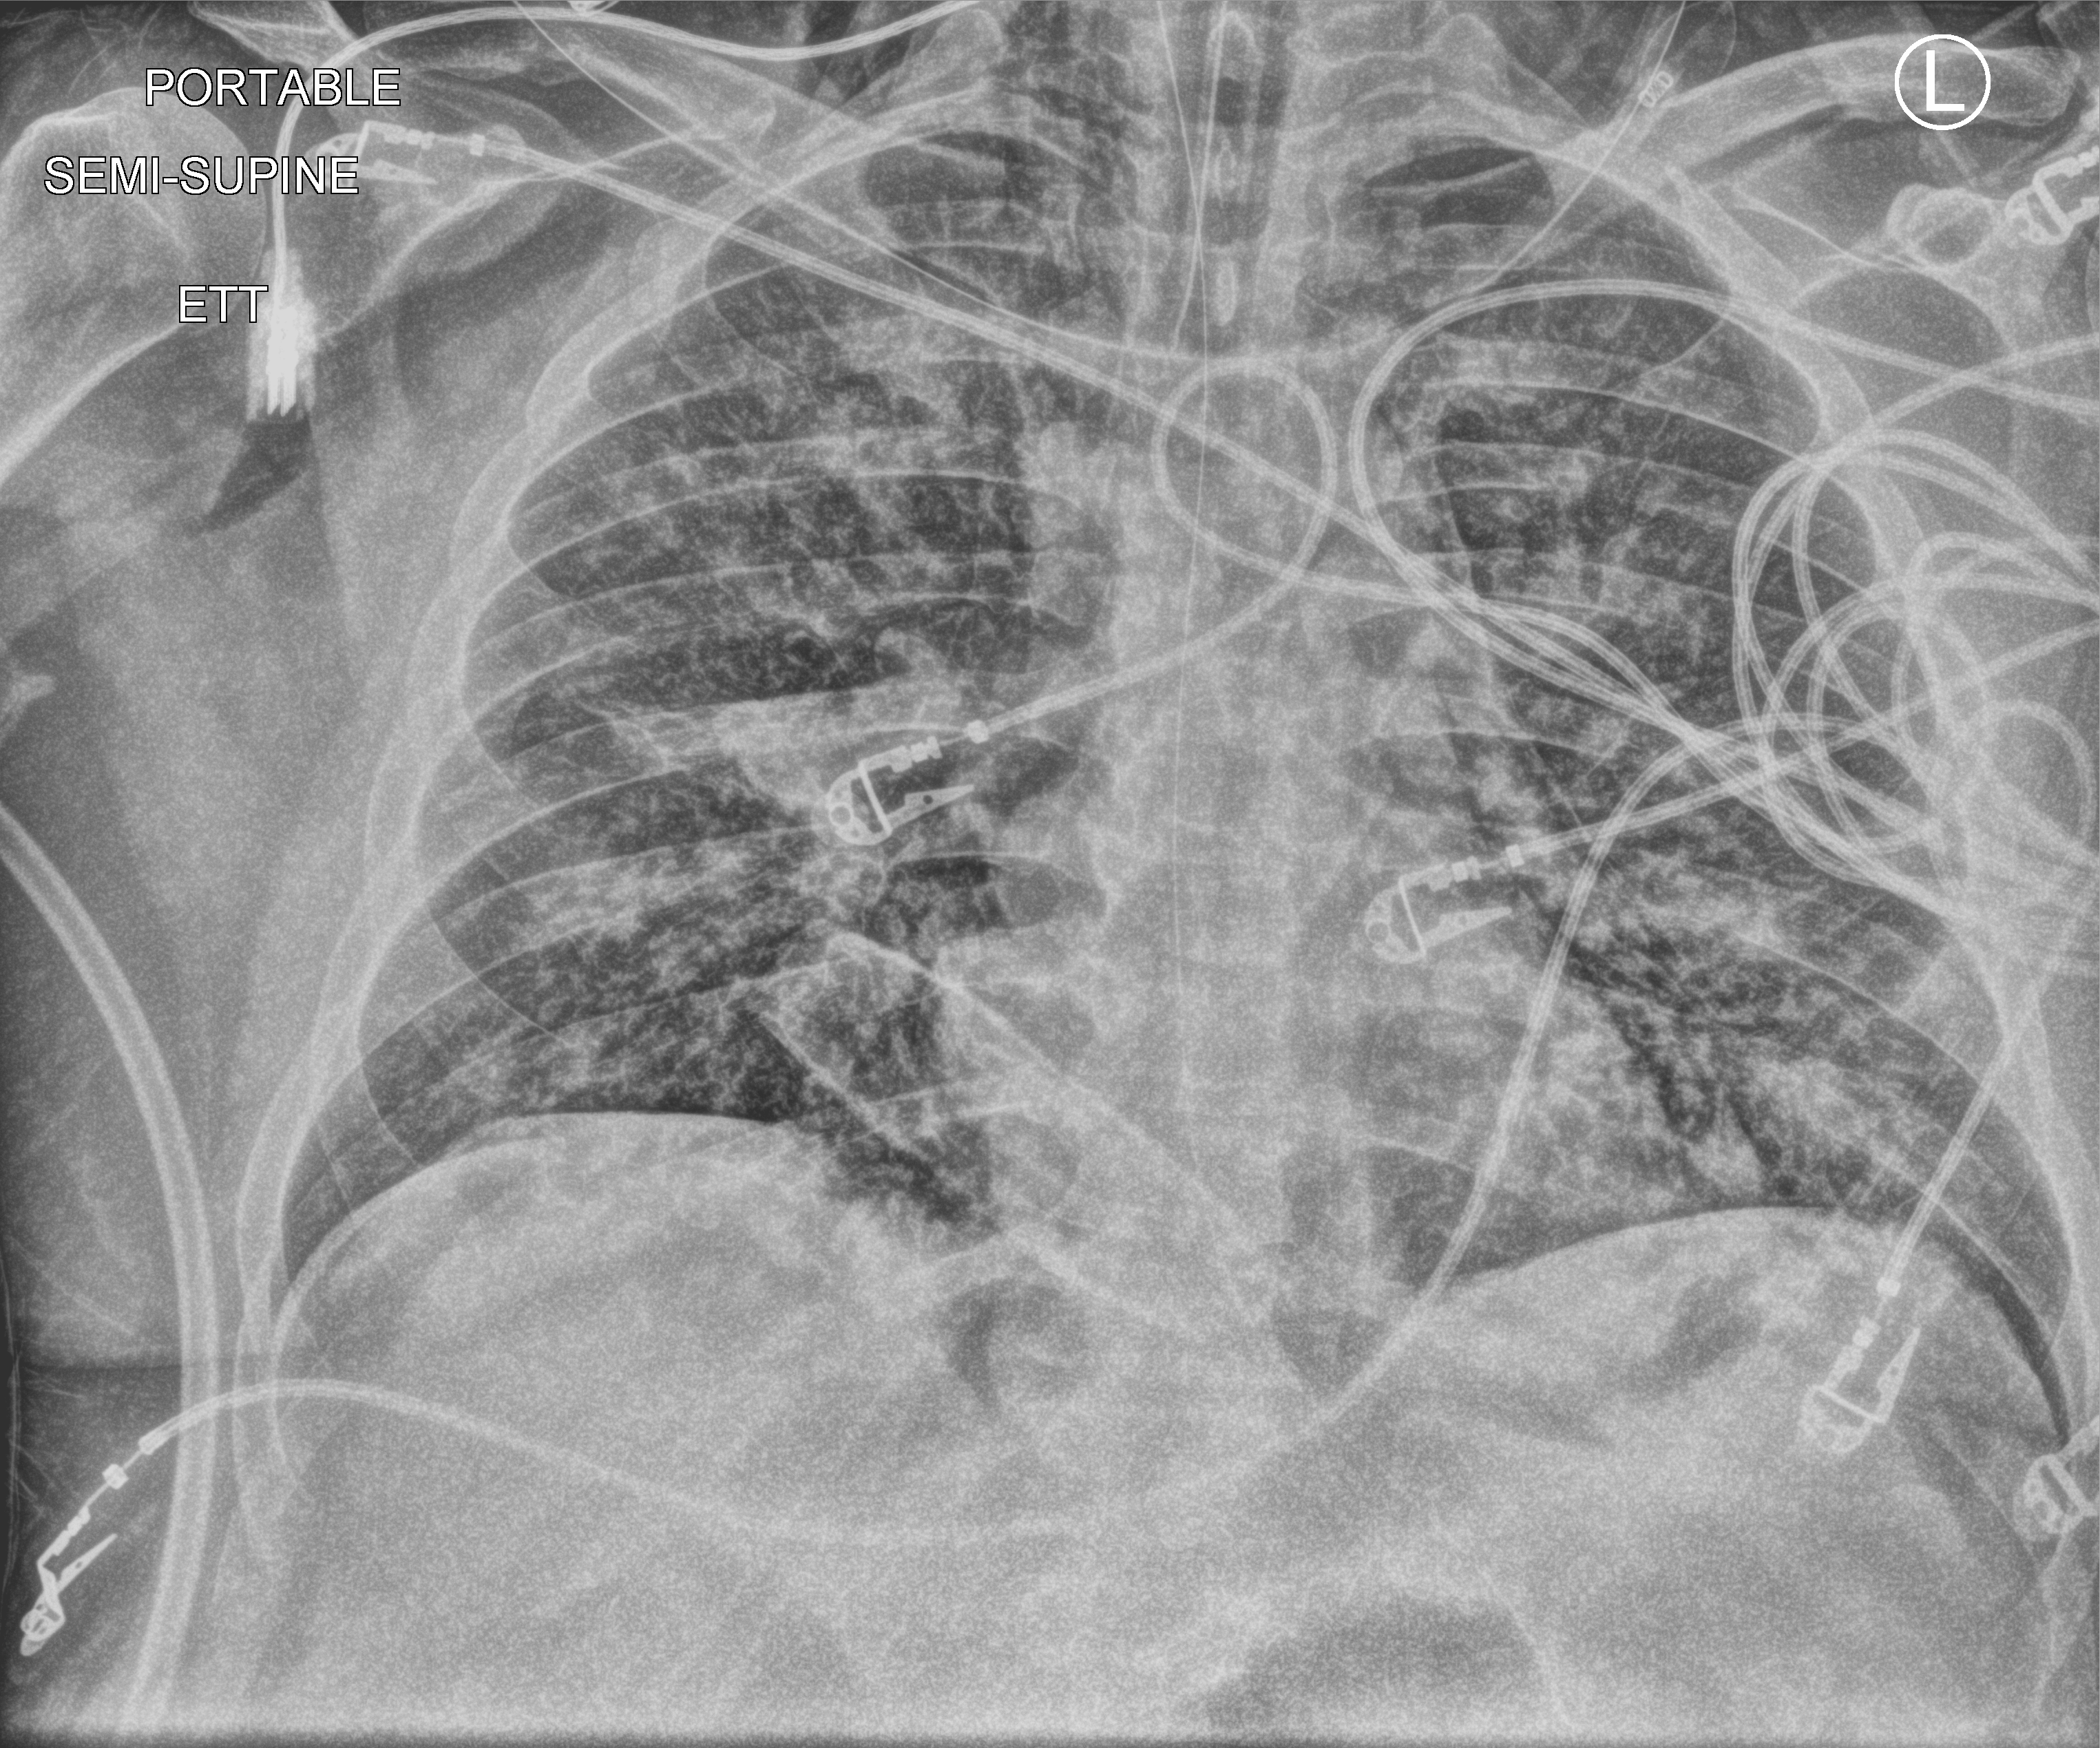
Chest X-ray (portable), anteroposterior (AP) projection. Adult patient hospitalised with COVID-19, age 18–59 years.
Hospital-stay facts (about this admission, not read from this image; timing relative to this image not recorded):
- admitted to intensive care during this hospital stay: yes
- length of hospital stay: 31 days
- mechanically ventilated during this hospital stay: yes